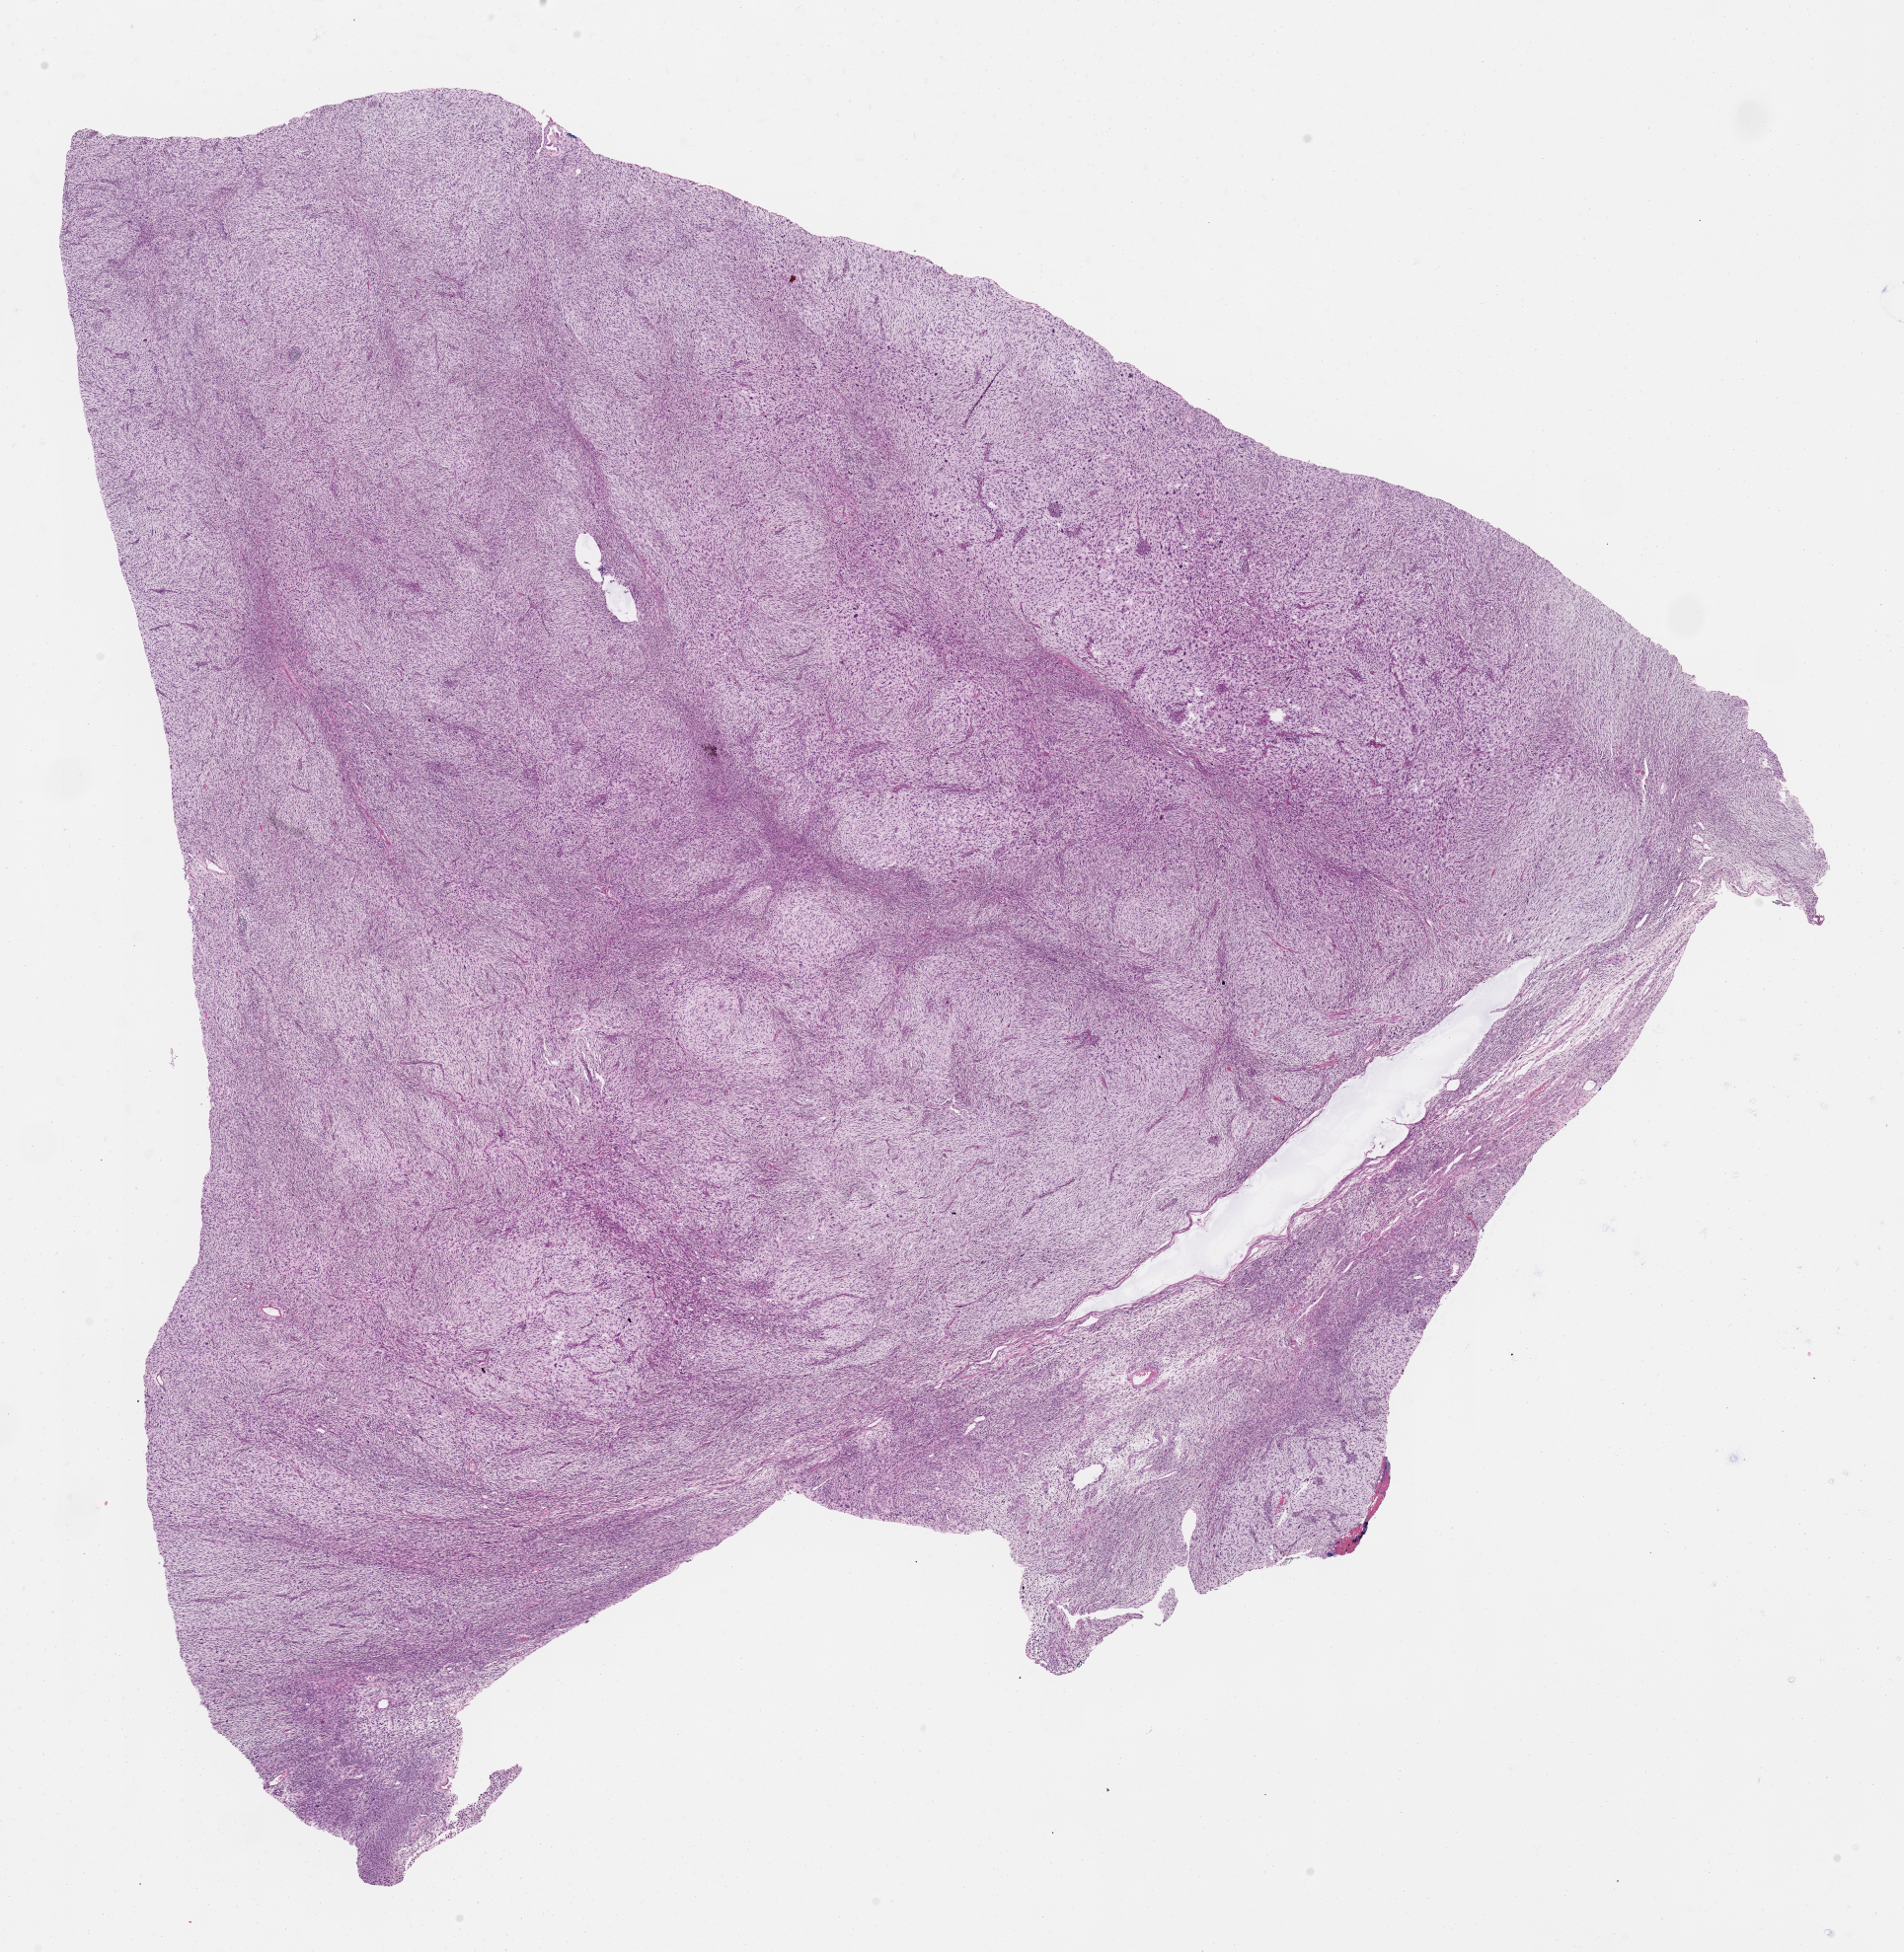
Whole-slide histology image, Hematoxylin and eosin (H&E) stained, low-resolution overview of the scanned area, about 15.6 x 16.0 mm (from a 40x scan). Formalin-fixed paraffin-embedded (FFPE) diagnostic section. Primary tumour sample from the connective, subcutaneous and other soft tissues. Male patient; age at initial diagnosis 61 years.
* diagnosis: Fibromyxosarcoma (connective, subcutaneous and other soft tissues of pelvis)